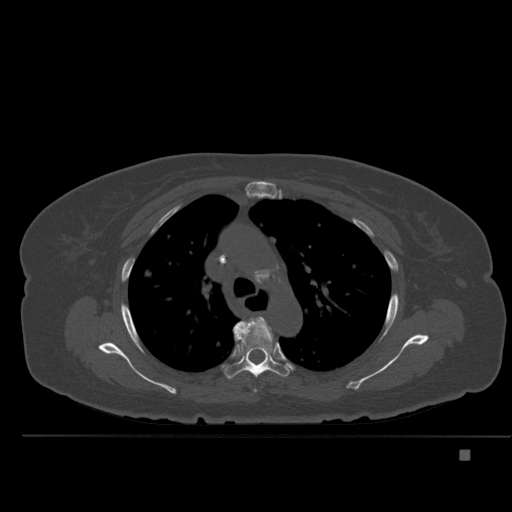
CT including the spine, one axial slice; position 357 of 477 along the scan axis; bone window (W 1800 / L 400 HU); 1.5 mm slice thickness; 512 × 512 image matrix. Female patient, age 74 years. From the clinical record (not read from this slice): primary cancer: colon.
Annotated regions visible in this slice (semi-automatically segmented with operator editing):
- T4 vertebra: bounding box <249,317,266,392> (left, top, right, bottom; pixels)
- T5 vertebra: <224,317,291,379>